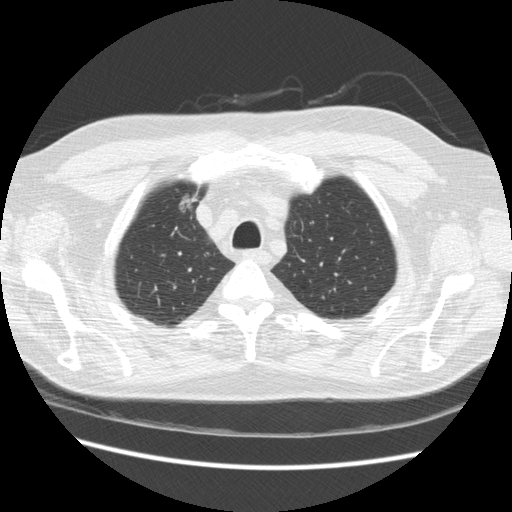
Low-dose screening chest CT, one axial slice. Position 191 of 234 along the scan axis. Reconstruction kernel STANDARD. 120 kVp. Lung window (W 1500 / L -600 HU). 2.5 mm slice thickness. 512 × 512 image matrix, field of view 360 × 360 mm.
Structures marked on this image (manually delineated by an expert):
- lesion 1 (tumor, upper lobe of right lung): box from (x=179, y=193) to (x=197, y=212) px